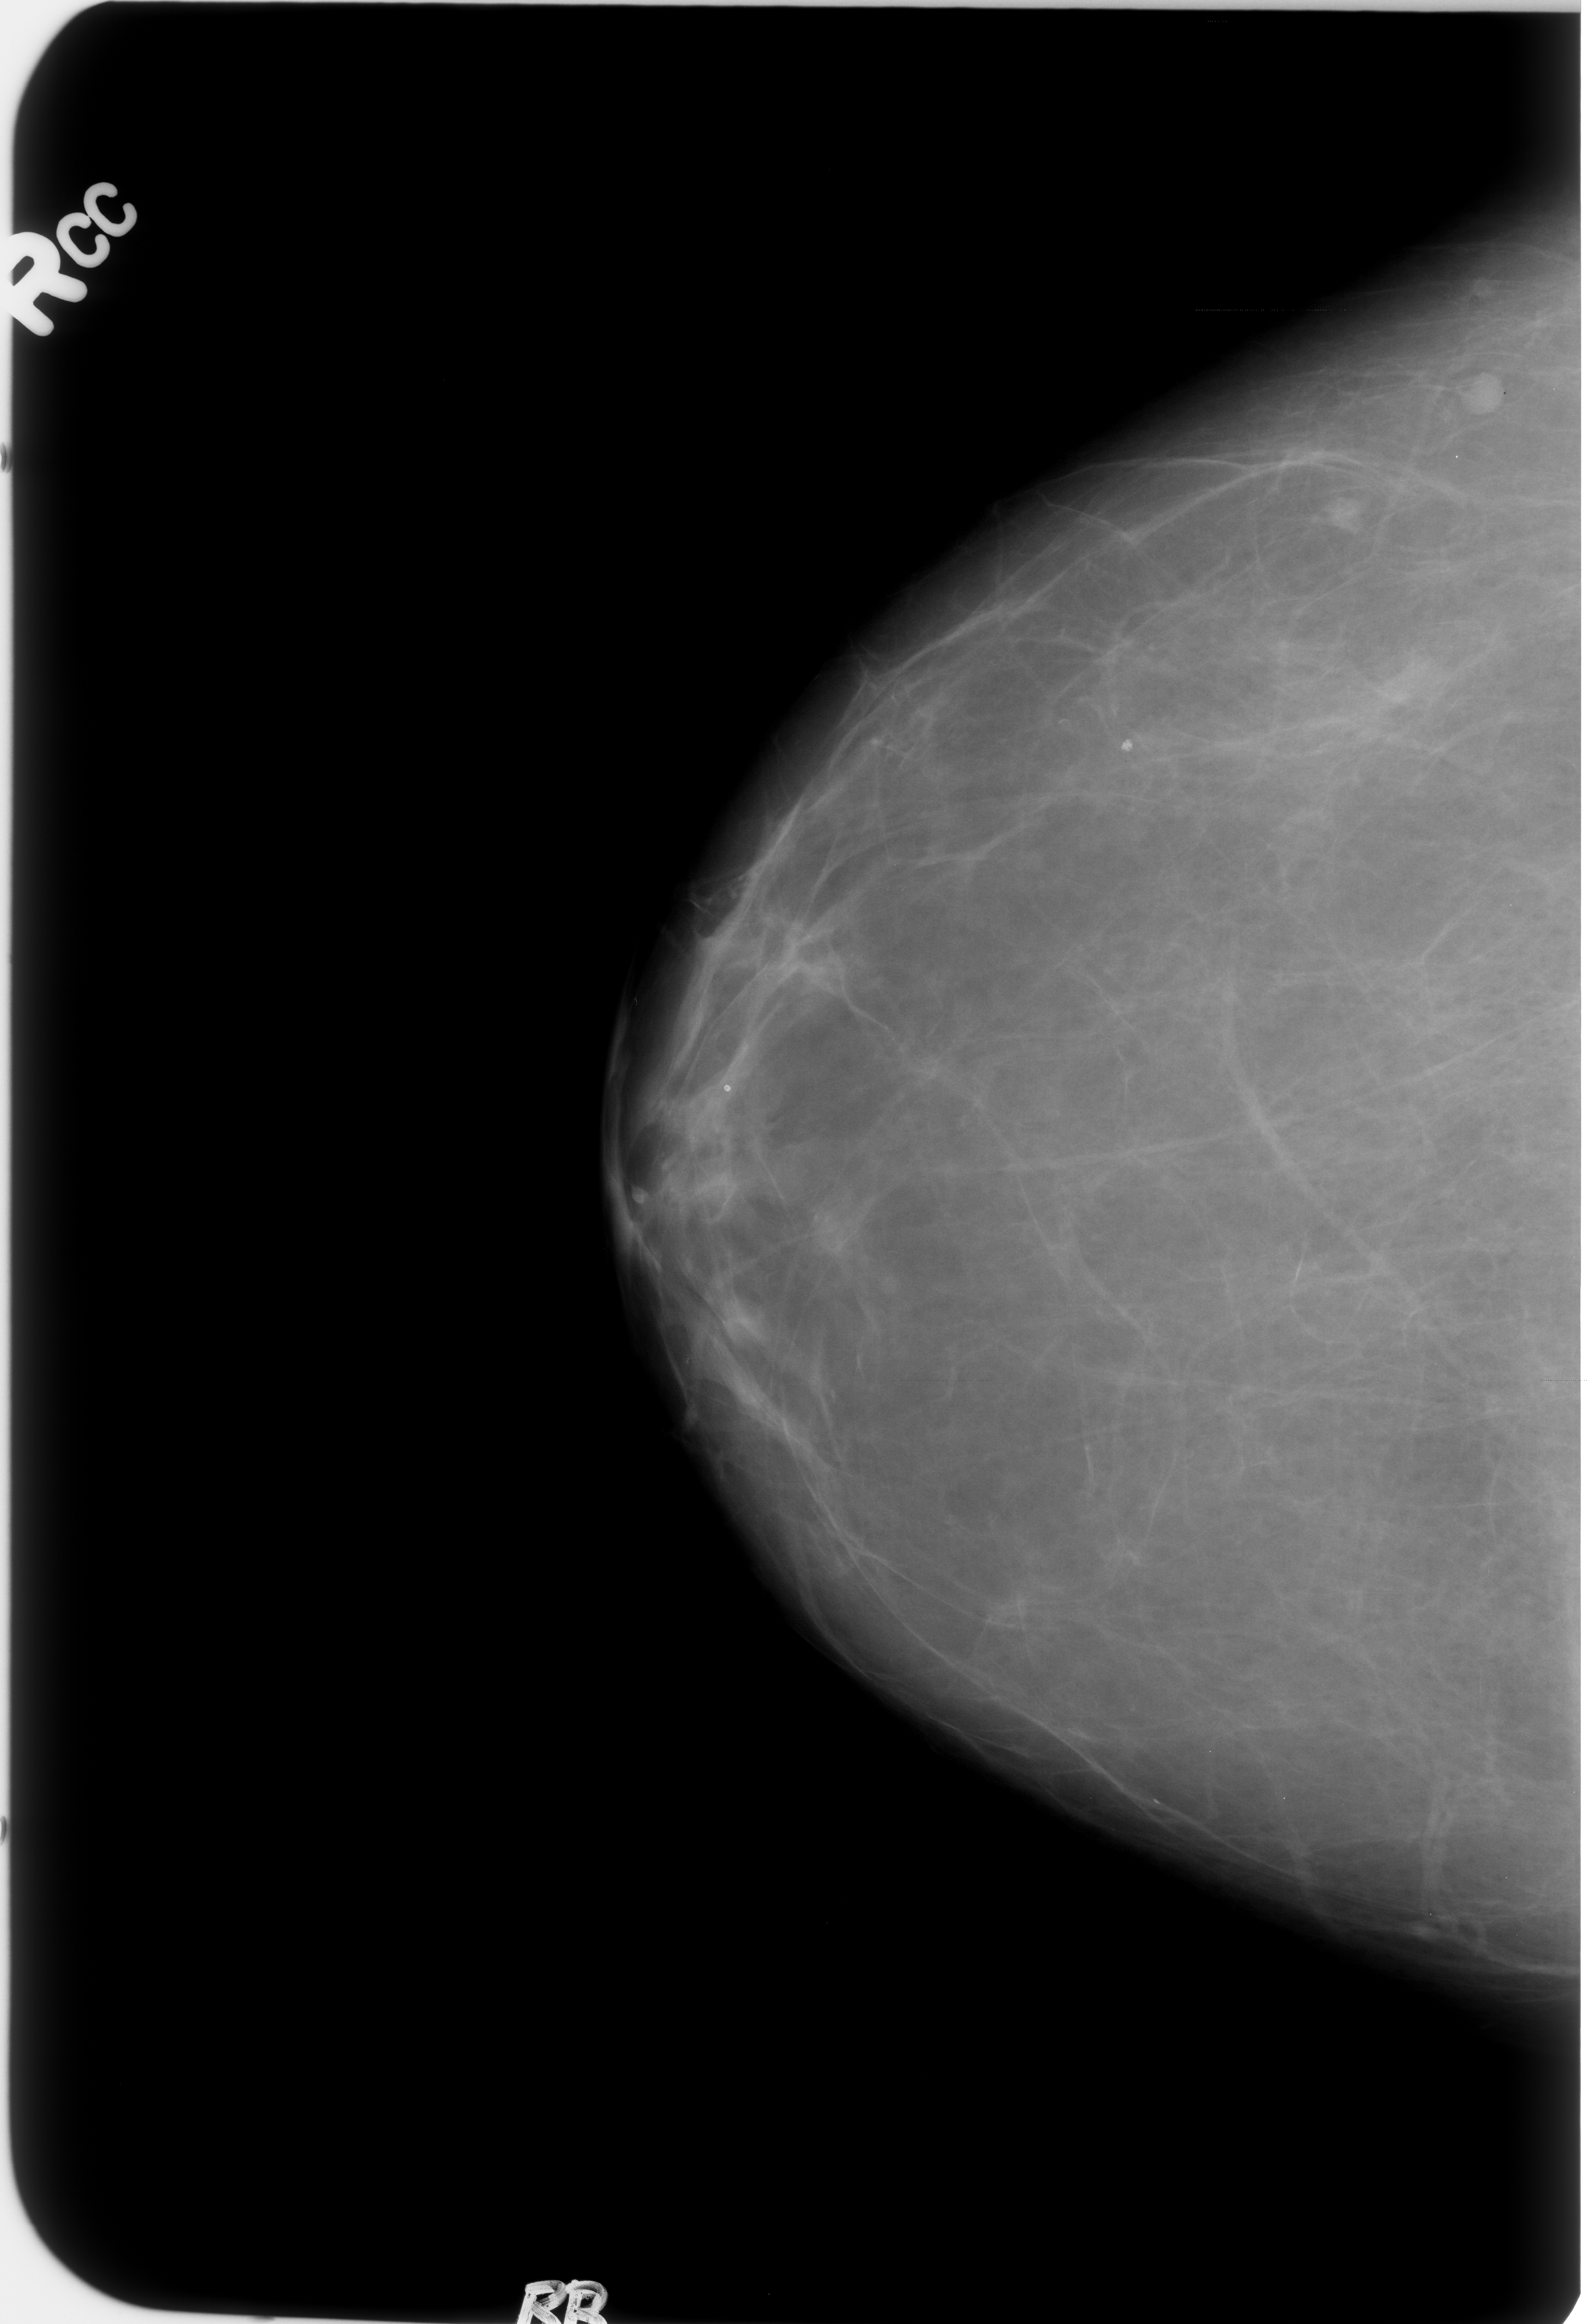
Digitized screen-film mammogram, right breast, CC view, breast composition: almost entirely fatty (BI-RADS density category 1 of 4).
Abnormality record for this image: Finding 1 of 3: mass, shape lymph node, margins circumscribed; BI-RADS assessment category 2; benign without callback (not worked up further). Finding 2 of 3: mass, shape lymph node, margins circumscribed; BI-RADS assessment category 2; benign; no additional work-up was recommended (benign without callback). Finding 3 of 3: mass, shape lymph node, margins circumscribed; BI-RADS assessment category 2; benign without callback (not worked up further).